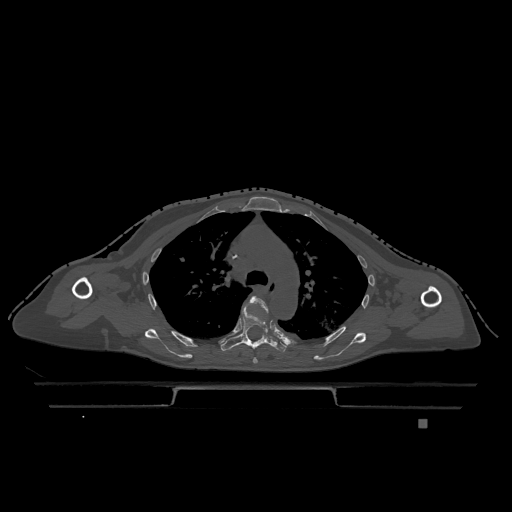
CT including the spine, one axial slice; slice 850 of 1317 in the series (ordered by position); bone window (W 1800 / L 400 HU); 512 × 512 image matrix, field of view 500 × 500 mm. Female patient, age 74 years. Case-level facts recorded for this patient, not image findings: primary cancer: lung; vertebrae with lytic lesions (as recorded): T1, T4, T5, T6, L4, L5.
Annotated regions visible in this slice (semi-automatic segmentation, software-assisted and operator-edited):
- T4 vertebra: box from (x=247, y=296) to (x=268, y=364) px
- T5 vertebra: (x=220, y=305)–(x=287, y=353)